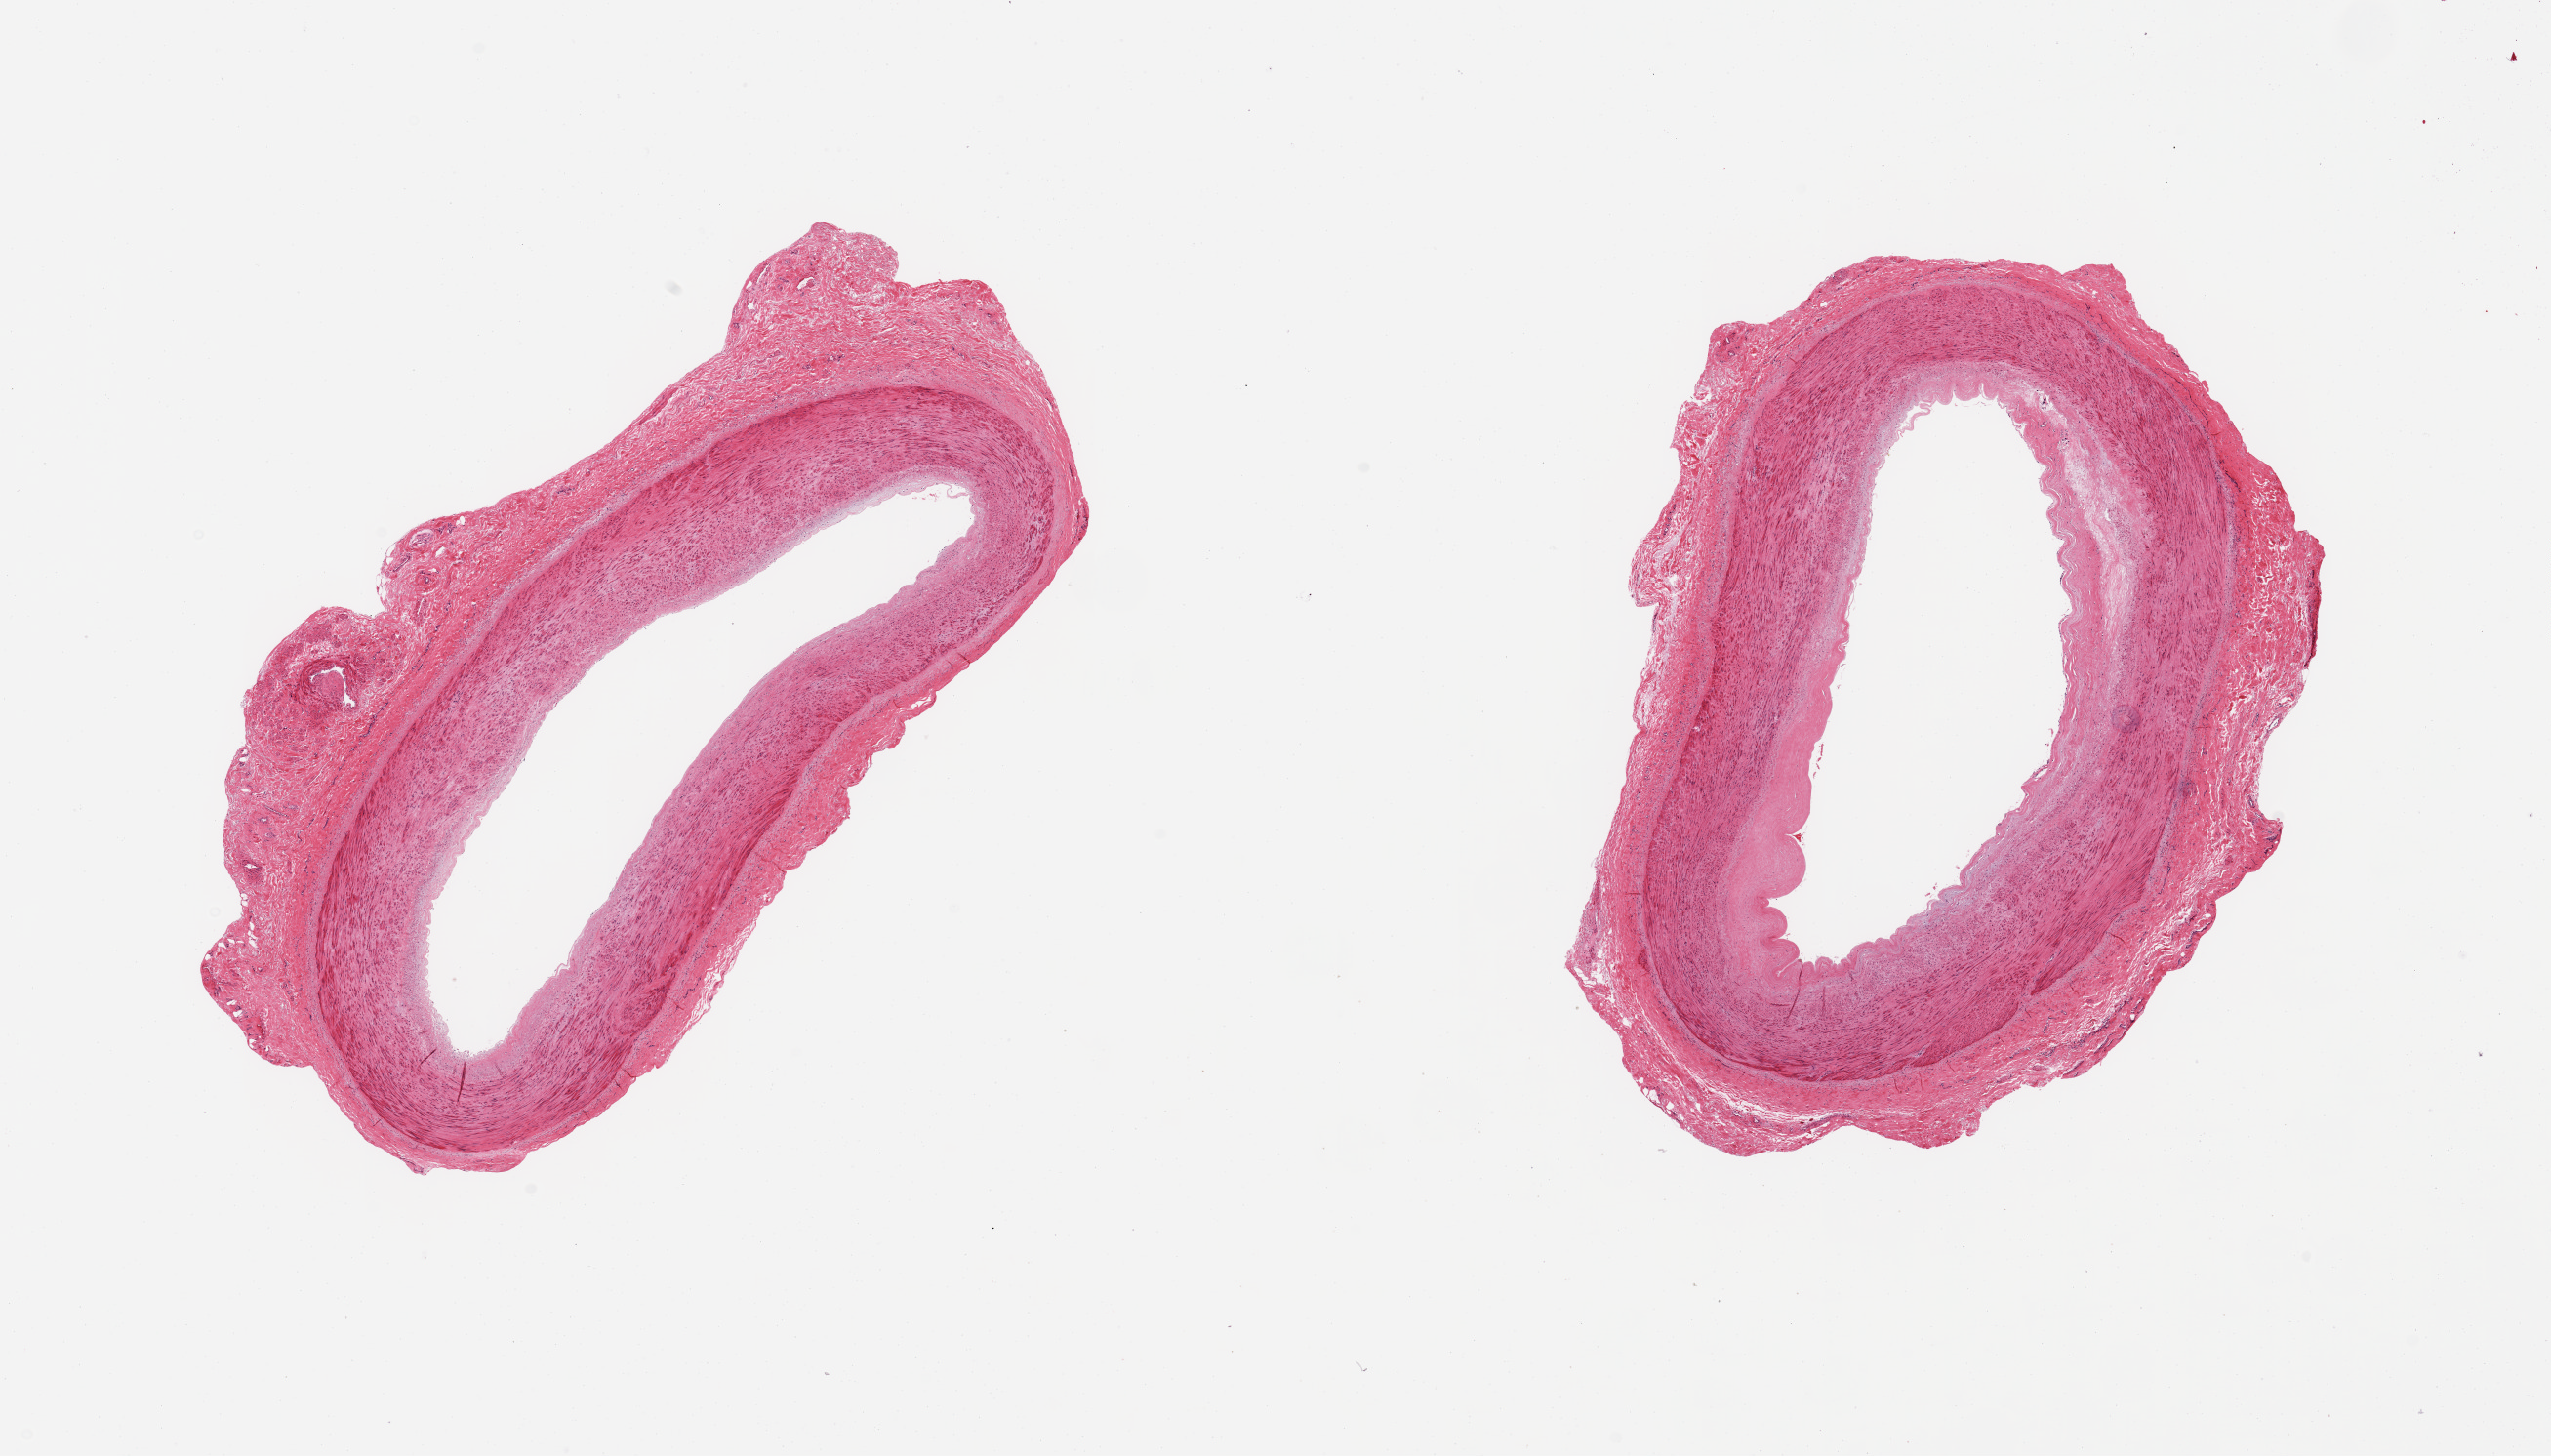
H&E whole-slide image, whole scanned area (about 20.7 x 11.8 mm) shown as a low-resolution overview, PAXgene-fixed paraffin-embedded (PFPE) section, section of tibial artery (target tissue), tissue donor sample. Male donor.
Review note (as recorded): 2 pieces, no atherosis, rim of fibrous tissue up to ~0.6mm.